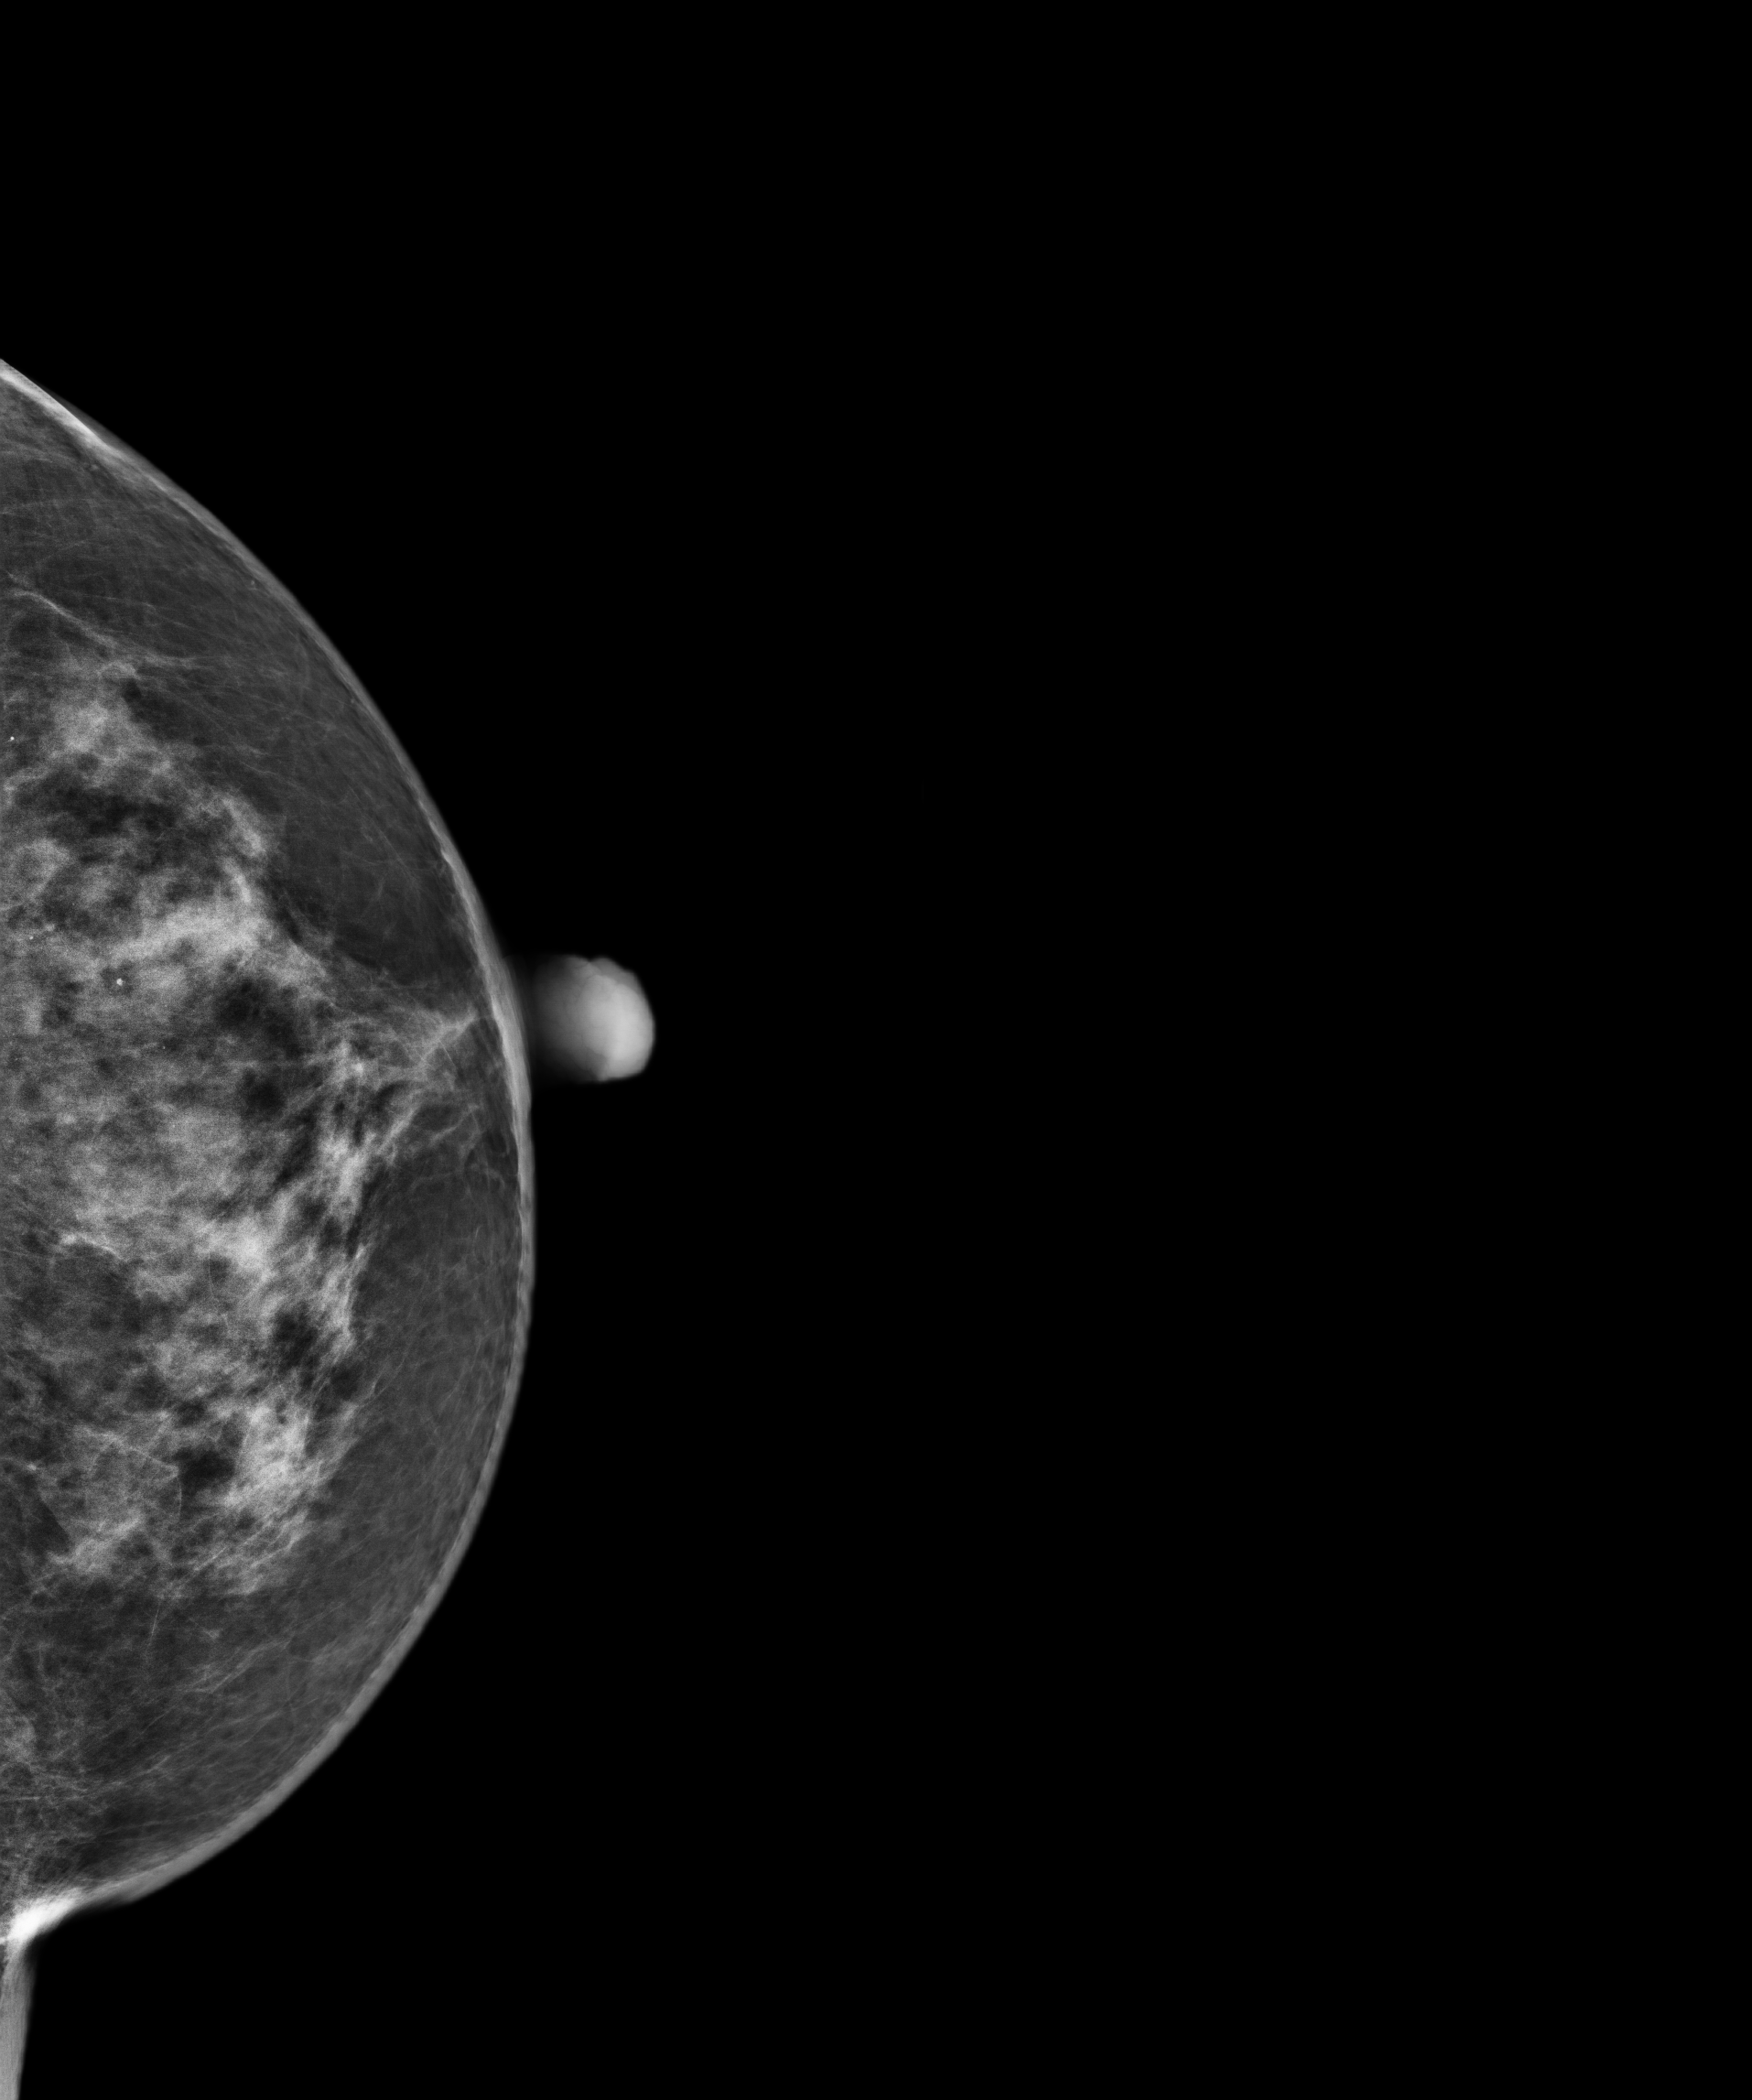
Annual screening mammography examination.
Image type: full-field digital mammogram. Breast: left. Projection: craniocaudal (CC) view.